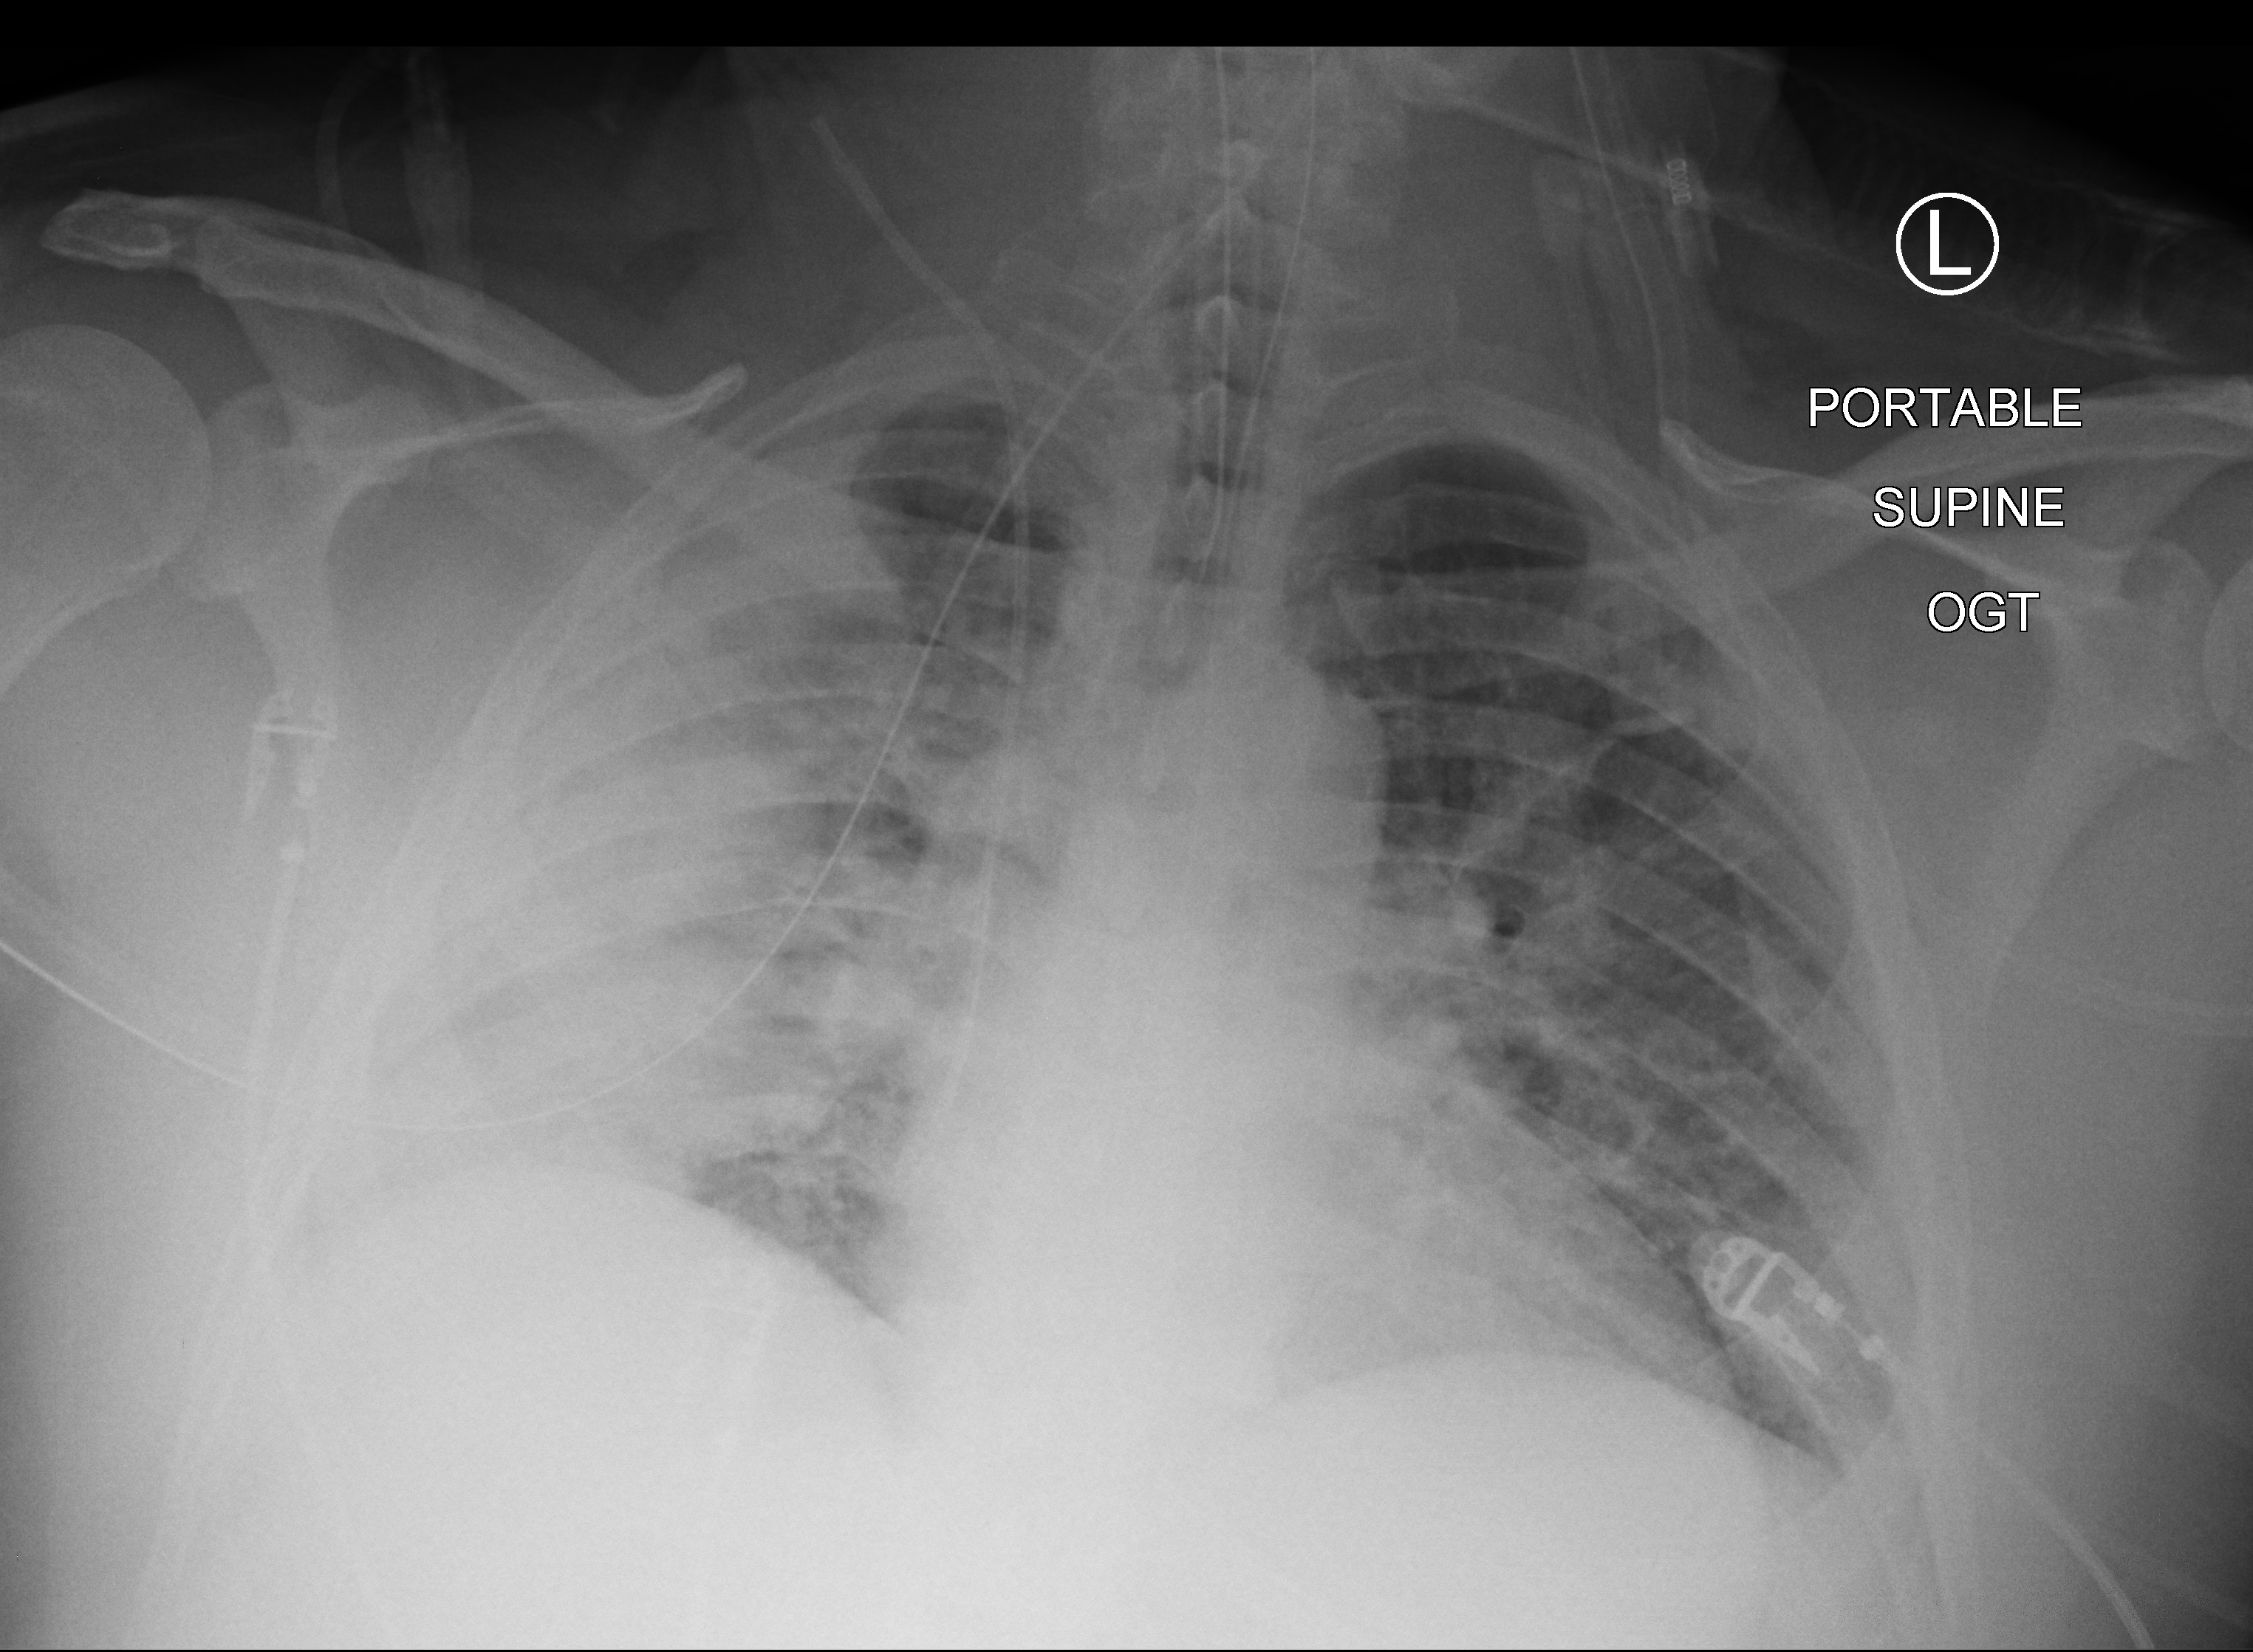
Chest X-ray (portable); anteroposterior (AP) projection. Male patient hospitalised with COVID-19, age 18–59 years.
Admission-level facts for this patient (not findings on this image; timing relative to this image not recorded):
- admitted to intensive care during this hospital stay: yes